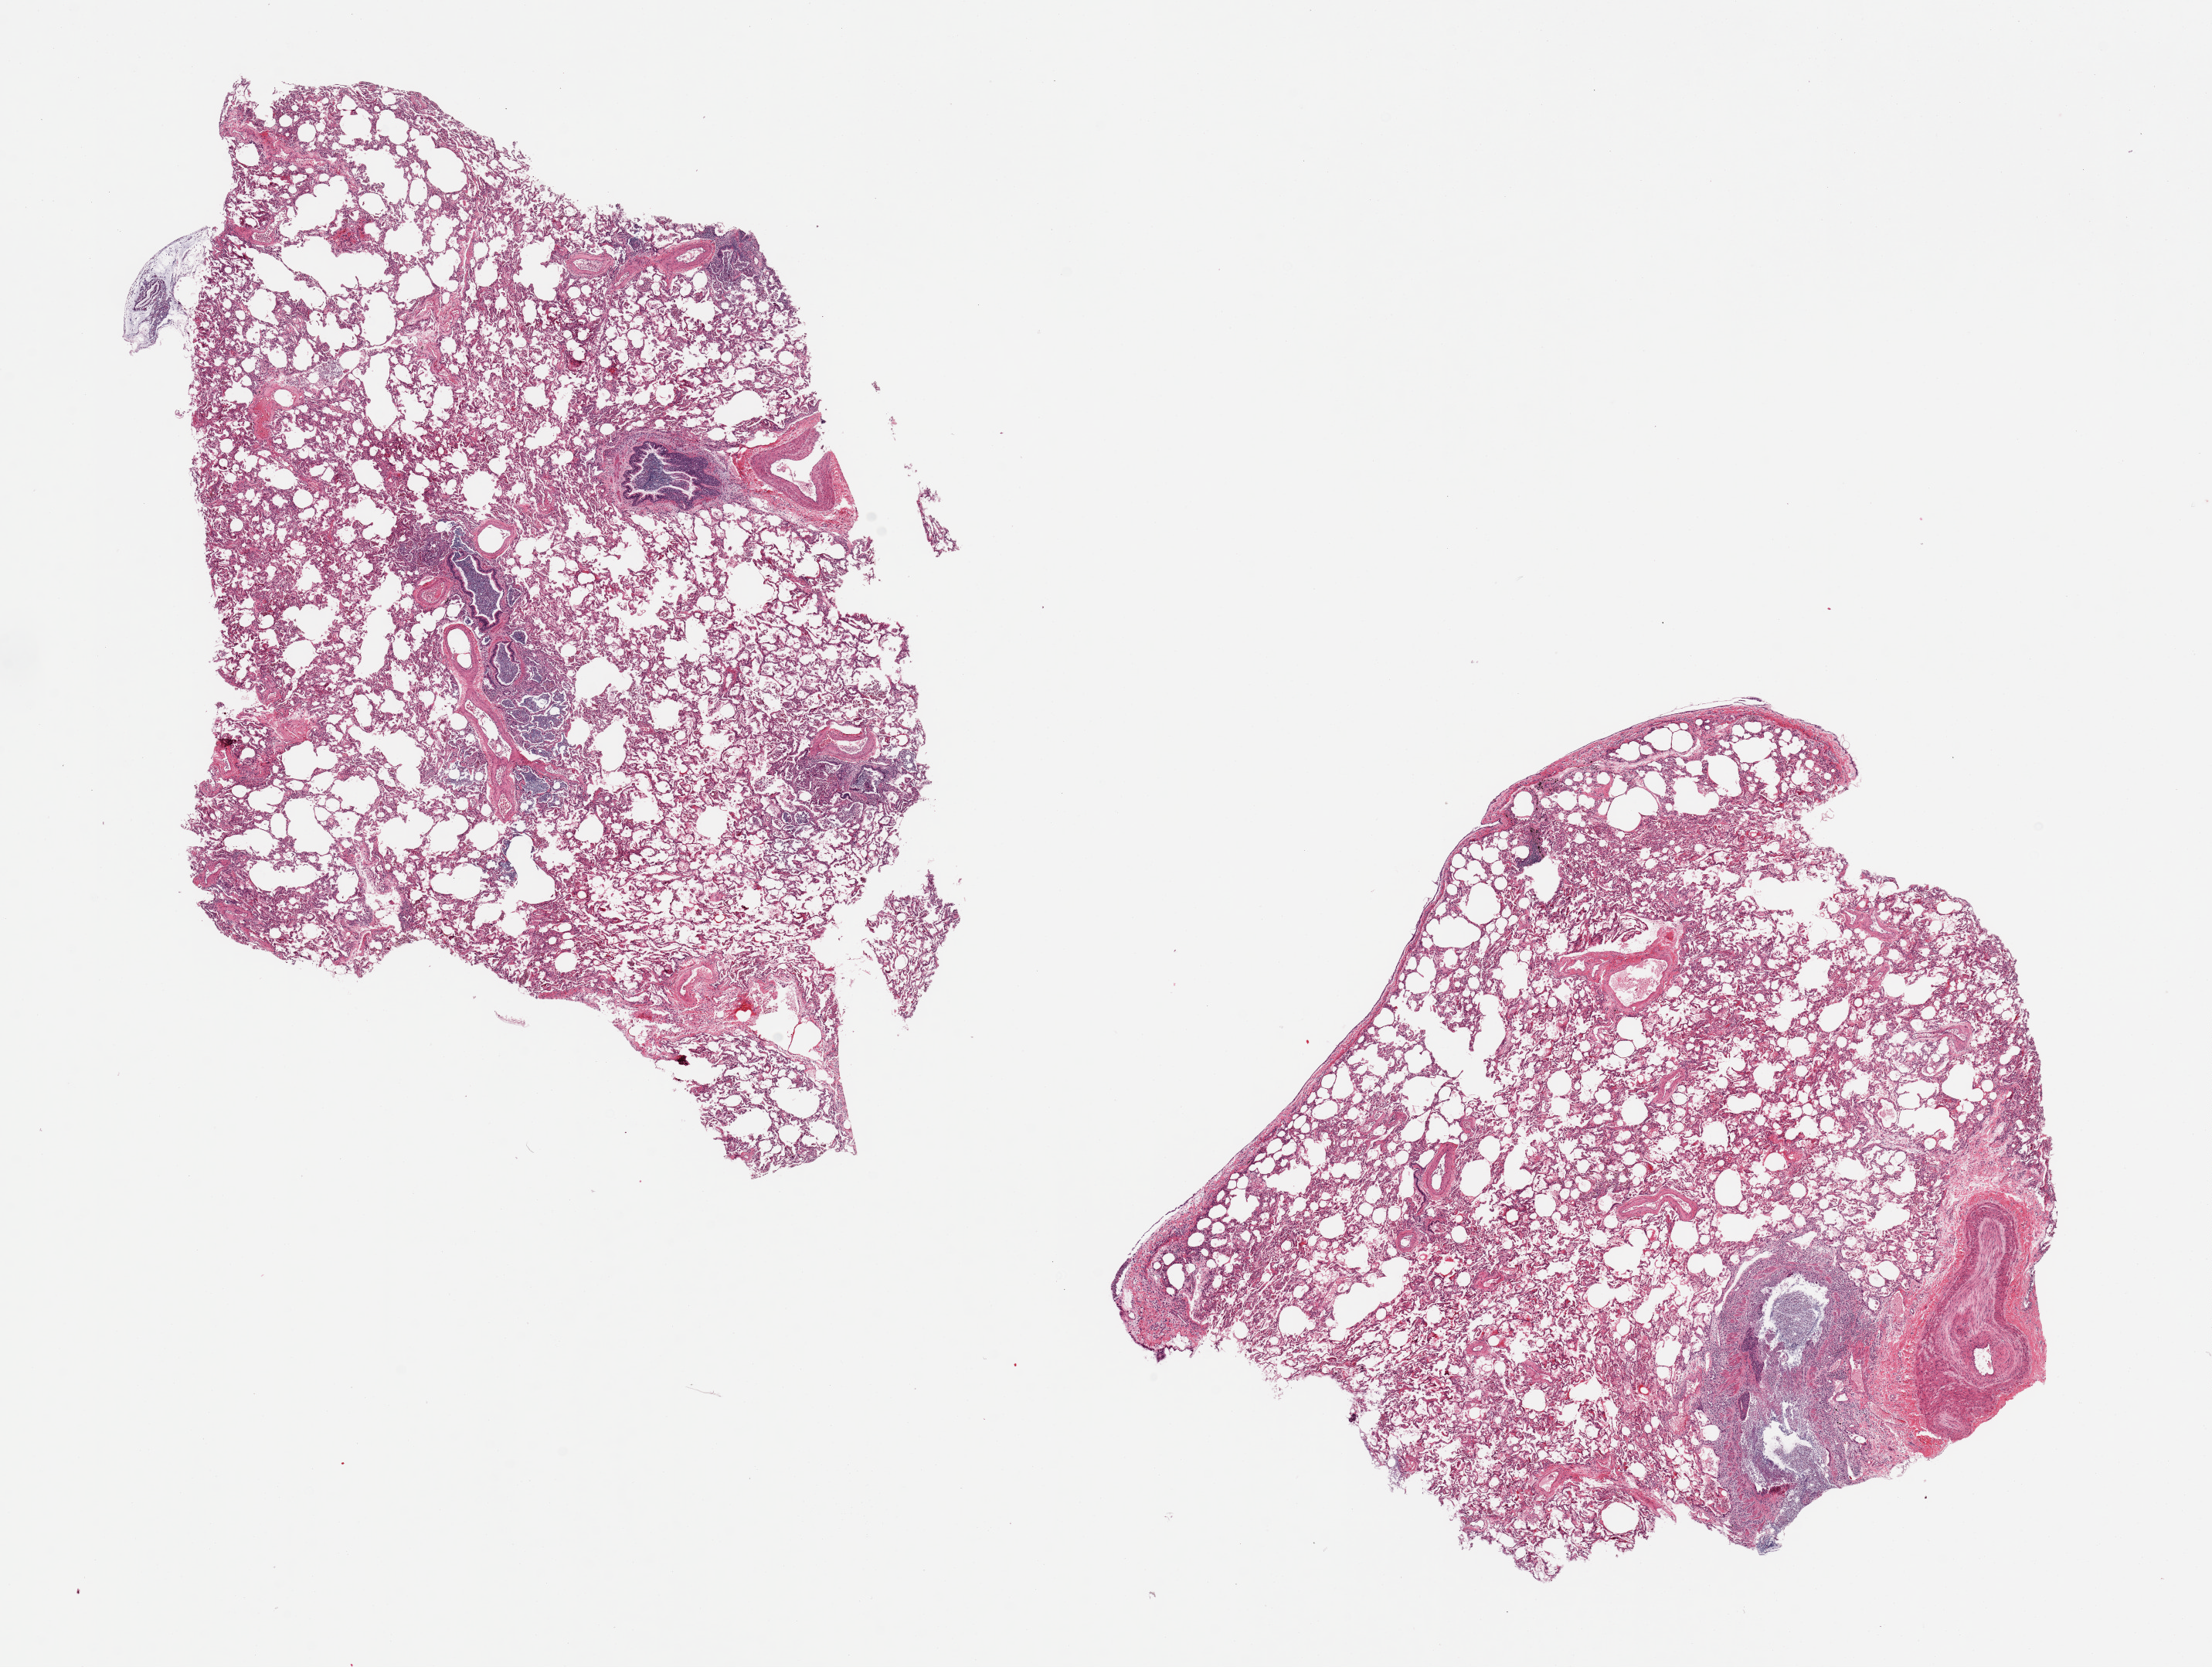
Whole-slide image, H&E stain, whole scanned area (about 22.6 x 17.1 mm) shown as a low-resolution overview. PAXgene-fixed, paraffin-embedded tissue. Sampled site (target tissue): lung. Tissue donor sample. Male donor.
* review note (as recorded): 2 pieces. Bronchial purulent exudates and adjacent pneumonia, <5% area. Heart failure cells. Partial pleural surface on one piece (please sample BELOW pleura)